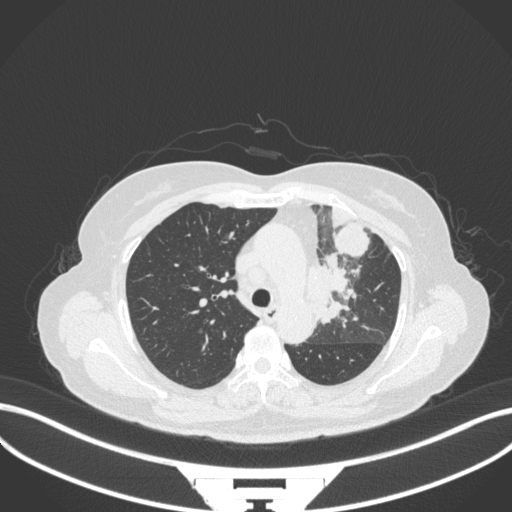
Chest CT, one axial slice. Slice 234 of 382 in the series (ordered by position). 120 kVp. Lung window (W 1500 / L -600 HU). 1 mm slice thickness. 512 × 512 image matrix. Female patient, age 64 years. From the clinical record (not read from this slice): clinical TNM (as recorded): T2a N2 M0.
Annotated regions visible in this slice (bounding box drawn by a radiologist):
- lung tumour (recorded histology: adenocarcinoma): bounding box <308,248,364,328> (left, top, right, bottom; pixels)
- lung tumour (recorded histology: adenocarcinoma): <334,218,373,259>